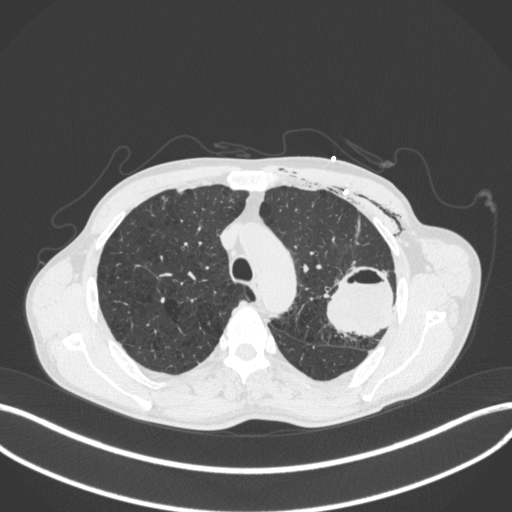
Chest CT, one axial slice. Slice 299 of 416 in the series (ordered by position). Reconstruction kernel B31f. 120 kVp. Lung window (W 1500 / L -600 HU). 512 × 512 image matrix, field of view 400 × 400 mm. Patient: male, 58 years. From the clinical record (not read from this slice): clinical TNM (as recorded): T3 N0 M0.
Annotated regions visible in this slice (rectangle marked by the reading radiologist):
- lung tumour (recorded histology: adenocarcinoma): bounding box (x1, y1, x2, y2) in pixels: (325, 262, 397, 341)